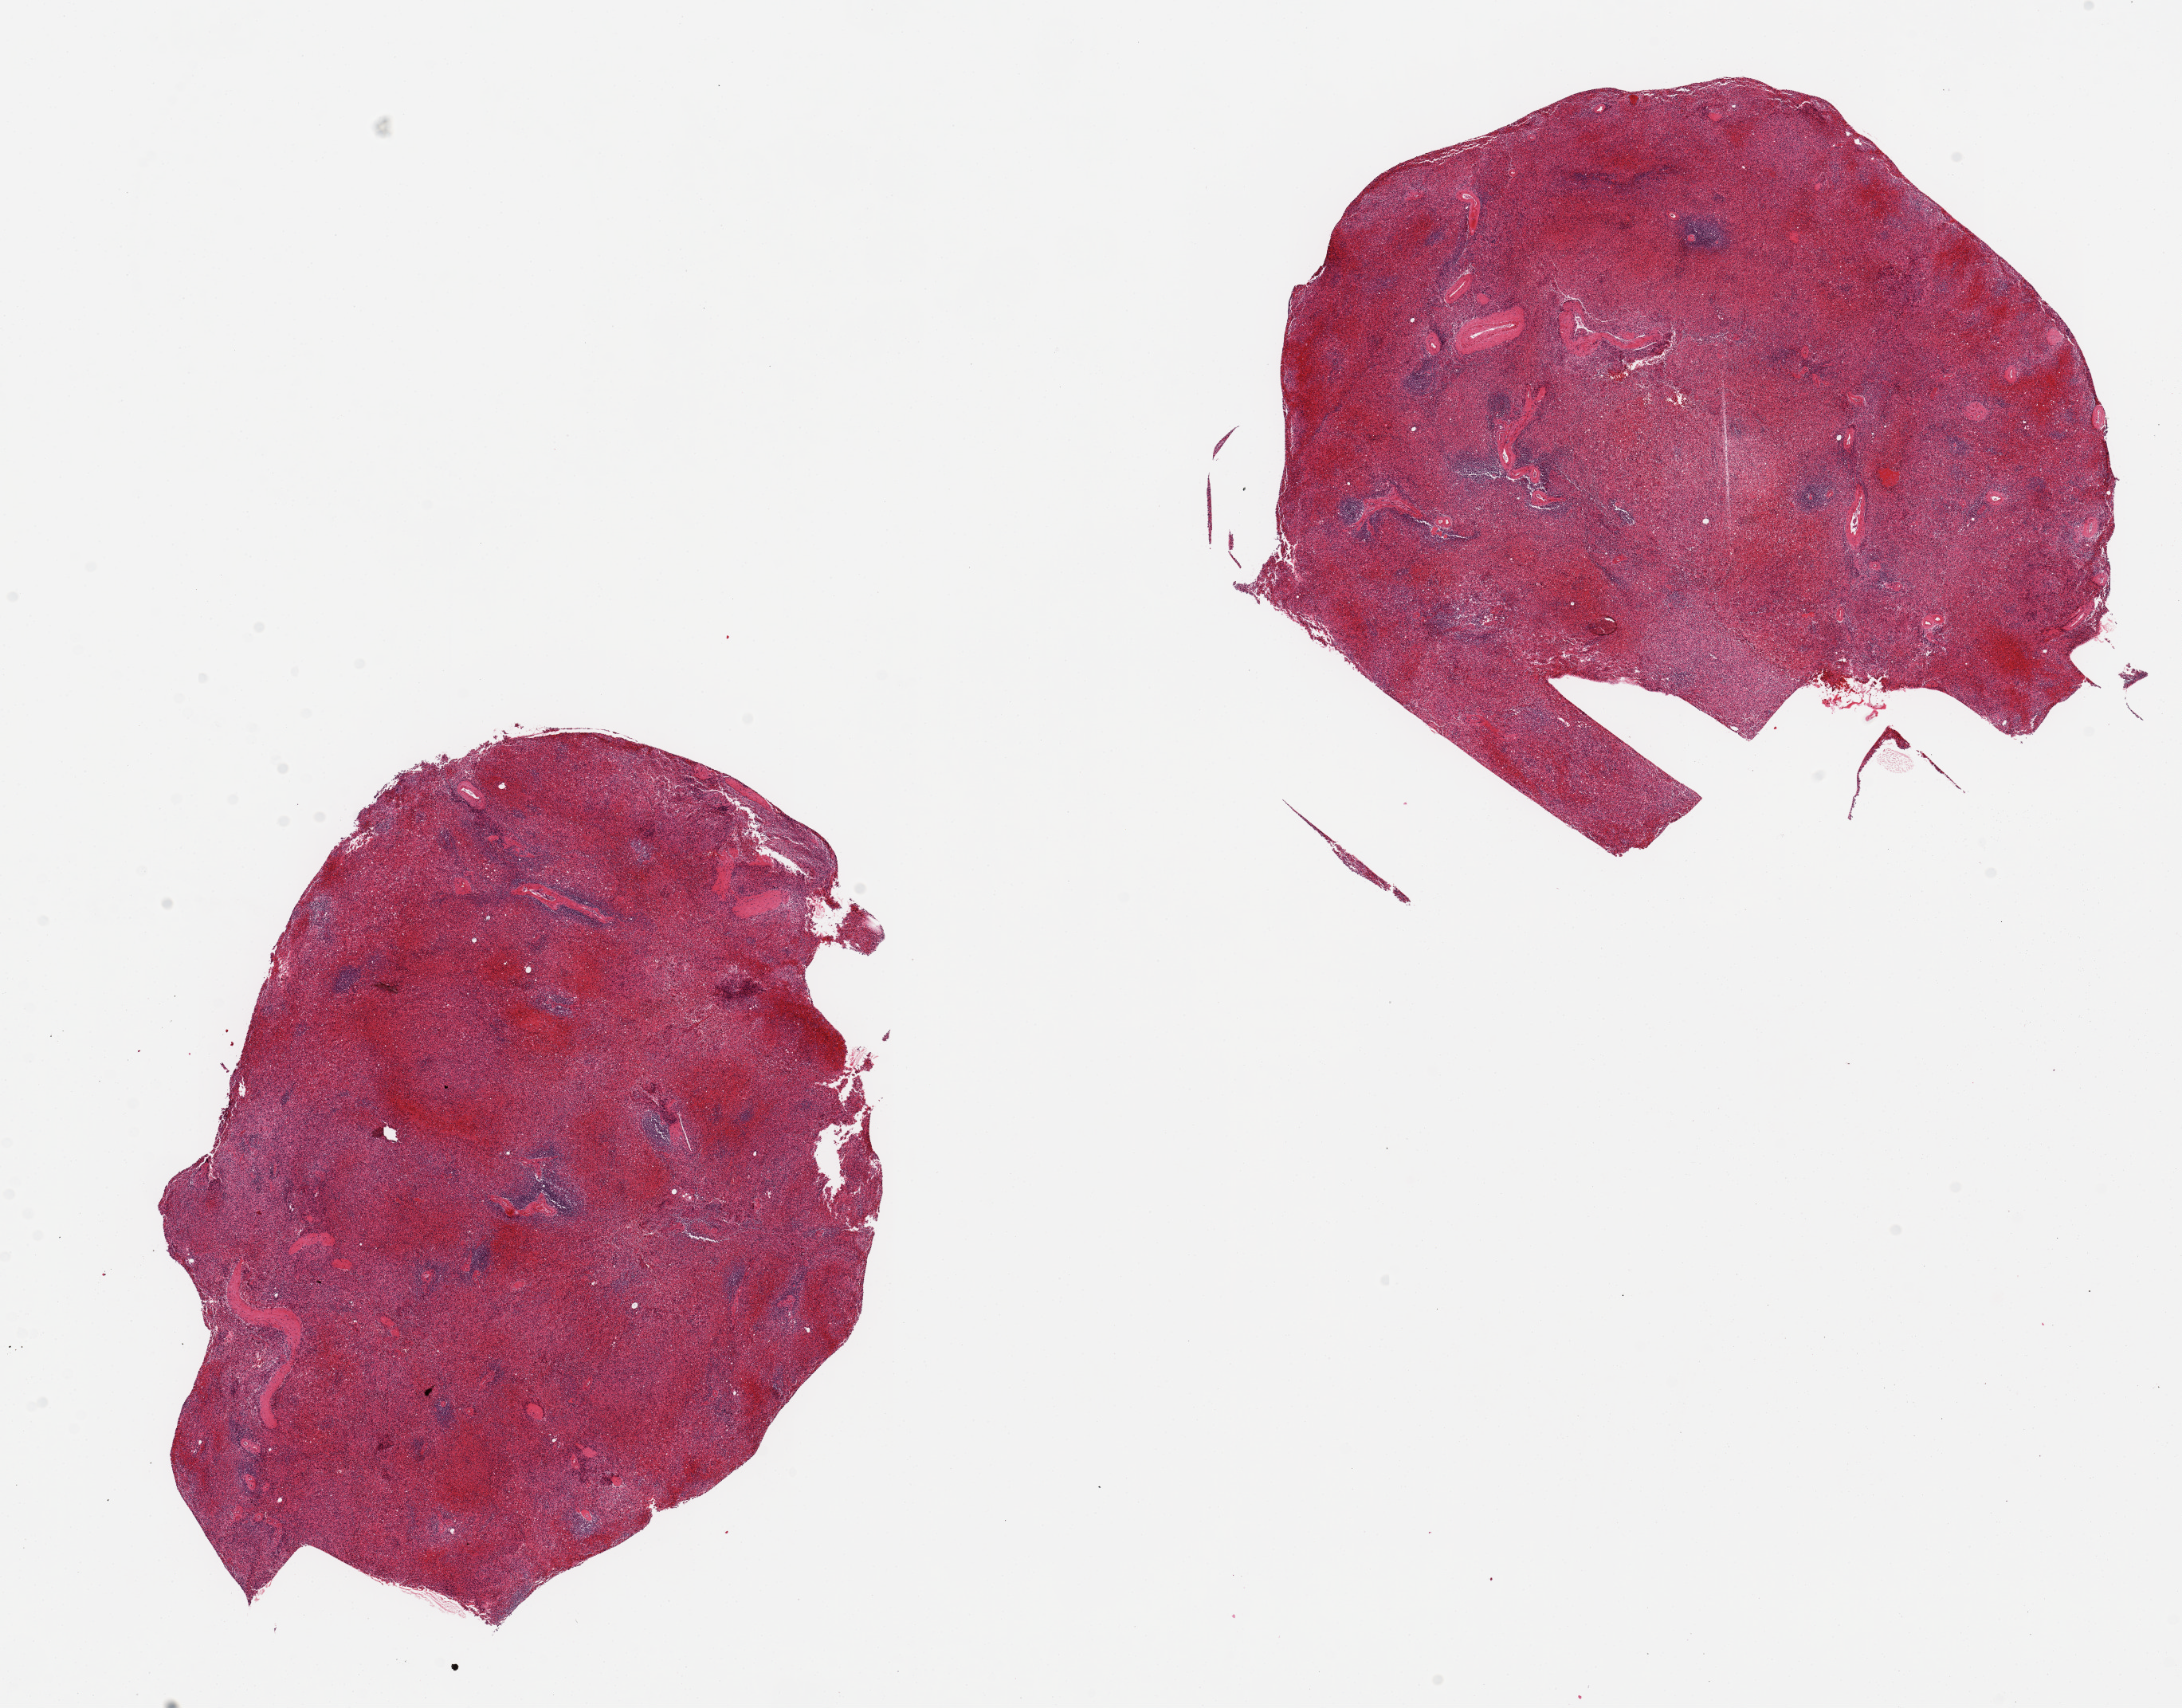
Whole-slide image, haematoxylin and eosin stain — low-resolution overview of the scanned area, about 21.7 x 17.0 mm; PAXgene-fixed paraffin-embedded (PFPE) section; sampled site (target tissue): spleen; tissue donor sample. Male donor.
Pathologist's review note for this sample: 2 pieces; congestion.